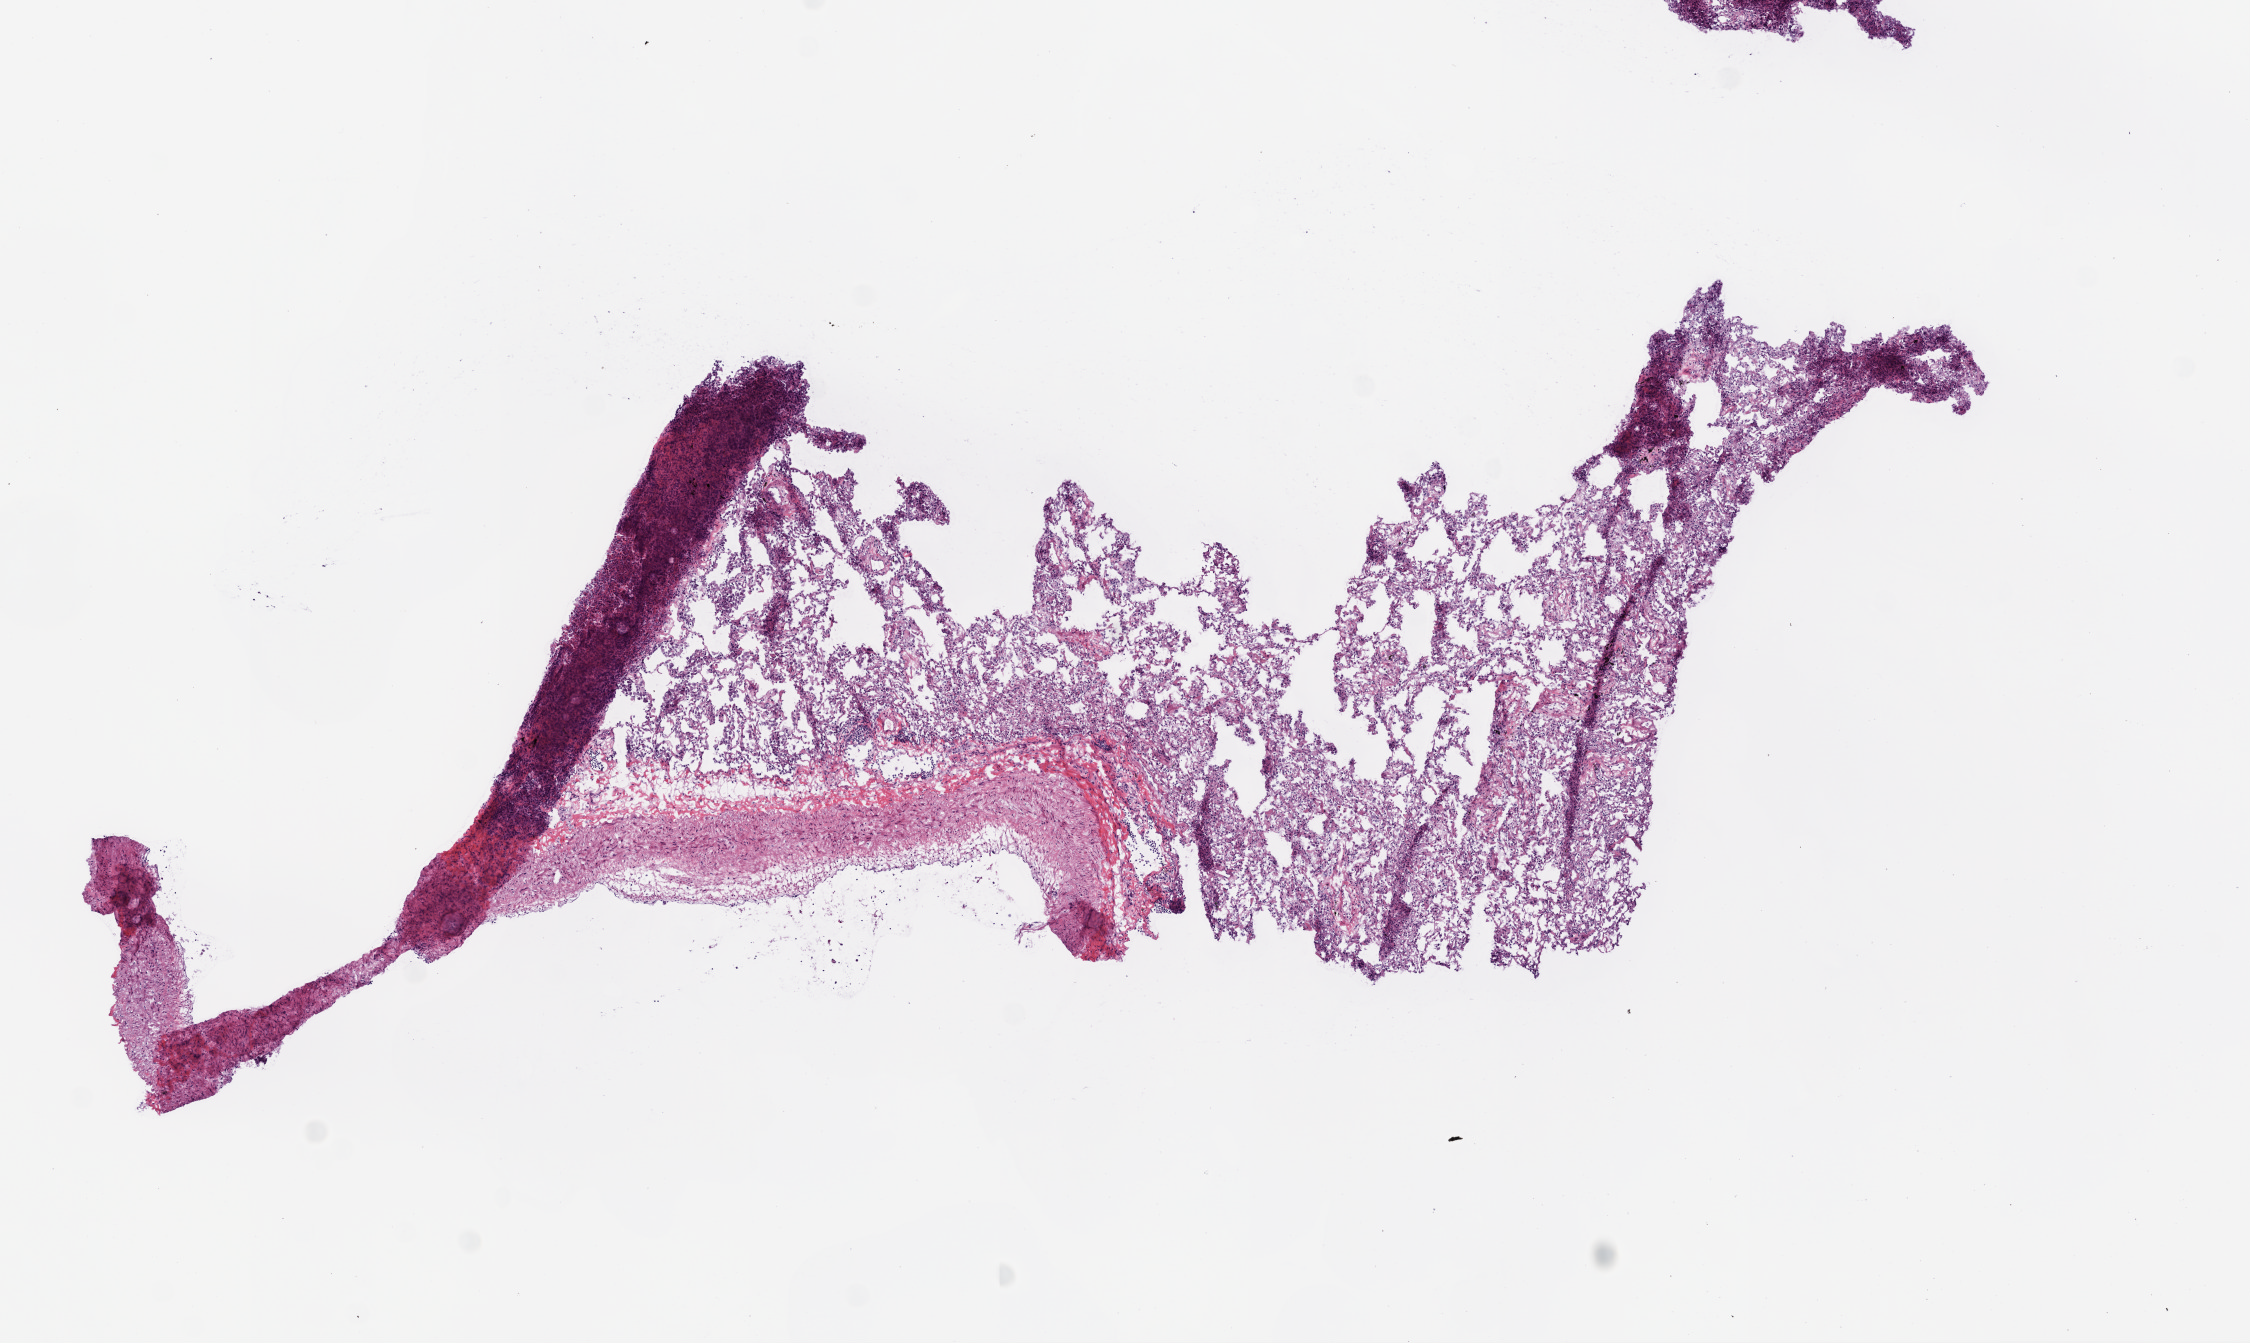
Whole-slide histology image, H&E-stained — low-resolution overview of the scanned area, about 9.0 x 5.4 mm (slide scanned at 20x); frozen section from the top of the tissue portion; solid tissue normal (non-tumour tissue) sample from the lung. Patient: male, age at initial diagnosis 52 years.
This section: solid tissue normal sample (biorepository sample class). Patient diagnosis: Squamous cell carcinoma, NOS (lower lobe, lung).